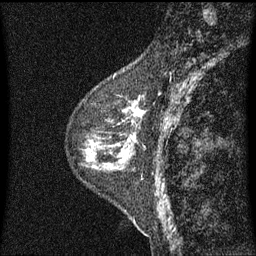
Breast MRI (dynamic contrast-enhanced), one sagittal slice. Position 19 of 60 along the scan axis. Dynamic contrast-enhanced series, image 2 of 3 at this slice position (ordered by acquisition). 1.5 T. TE 4.2 ms, TR 8 ms. 2 mm slice thickness. 256 × 256 image matrix, field of view 200 × 200 mm. Female patient, age 48 years.
Annotated regions visible in this slice (semi-automatic segmentation, software-assisted and operator-edited):
- analysis volume of interest (the breast-tissue region the enhancement analysis was run in; not a lesion): bounding box (x1, y1, x2, y2) in pixels: (103, 74, 145, 139)
- tumour enhancement mask (voxels above the 70 % enhancement threshold inside the analysis volume of interest): (111, 96, 145, 139)